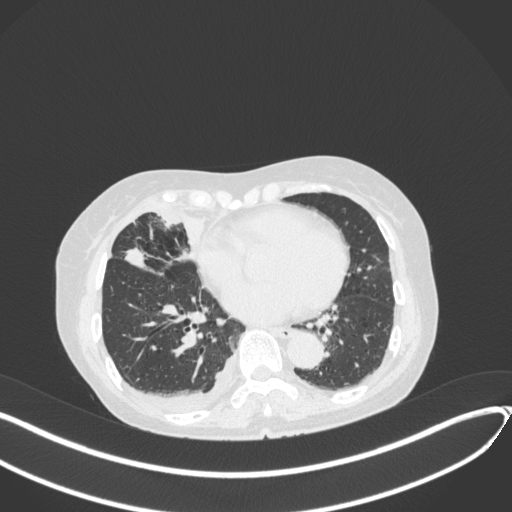
Chest CT, one axial slice. Slice 156 of 418 in the series (ordered by position). 120 kVp. Lung window (W 1500 / L -600 HU). 1 mm slice thickness. 512 × 512 image matrix, field of view 400 × 400 mm. Patient: female, 75 years. From the clinical record (not read from this slice): clinical TNM (as recorded): T2a N3 M0.
Annotated regions visible in this slice (bounding box drawn by a radiologist):
- lung tumour (recorded histology: adenocarcinoma): bounding box [x1, y1, x2, y2] px = [123, 245, 149, 270]